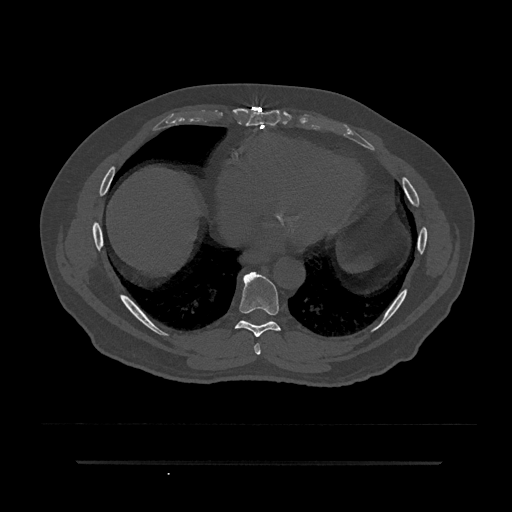
CT including the spine, one axial slice; slice 424 of 797 in the series (ordered by position); reconstruction kernel Br40s/3; 120 kVp; bone window (W 1800 / L 400 HU); 512 × 512 image matrix. Patient: male, 59 years. From the clinical record (not read from this slice): primary cancer: bile ducts; vertebrae with lytic lesions (as recorded): T10.
Annotated regions visible in this slice (semi-automatically segmented with operator editing):
- T7 vertebra: bounding box [x1, y1, x2, y2] px = [254, 343, 261, 355]
- T8 vertebra: [235, 271, 281, 337]